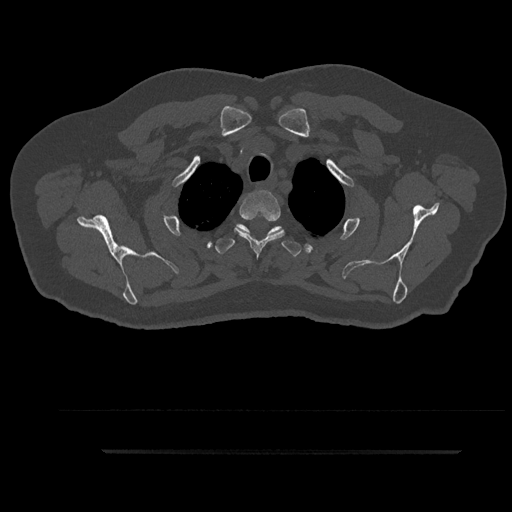
CT including the spine, one axial slice; slice 746 of 797 in the series (ordered by position); reconstruction kernel Br40s/3; 120 kVp; bone window (W 1800 / L 400 HU); 0.5 mm slice thickness; 512 × 512 image matrix, field of view 432 × 432 mm. Patient: male, 63 years. Case-level facts recorded for this patient, not image findings: primary cancer: renal.
Annotated regions visible in this slice (semi-automatically segmented with operator editing):
- T2 vertebra: box from (x=234, y=190) to (x=285, y=258) px
- T3 vertebra: (x=215, y=224)–(x=302, y=257)